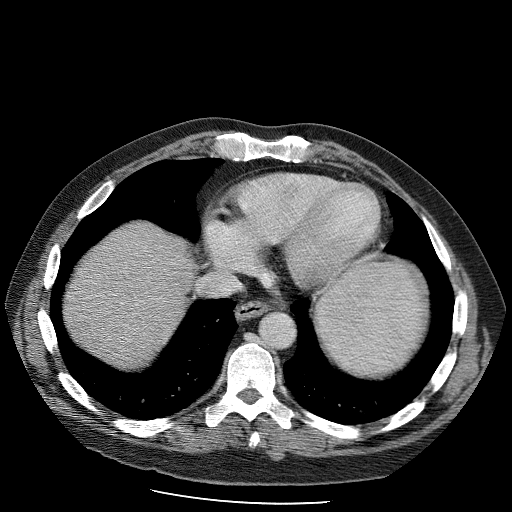
Contrast-enhanced abdominal CT (liver protocol), one axial slice. Slice 93 of 98 in the series (ordered by position). Soft-tissue window (W 400 / L 40 HU). 2.5 mm slice thickness. 512 × 512 image matrix, field of view 400 × 400 mm. From the clinical record (not read from this slice): diagnosis: hepatocellular carcinoma (patient treated with transarterial chemoembolisation; whether this scan precedes or follows treatment is not stated here); TNM stage (as recorded): Stage-II; Child-Pugh class: B; tumour differentiation: moderately differentiated; tumour nodularity: uninodular.
Structures marked on this image (semi-automatically segmented with operator editing):
- liver parenchyma outside the tumour (the mass and vessels are separate outlines, so this box may not span the whole liver): bounding box <68,226,190,354> (left, top, right, bottom; pixels)